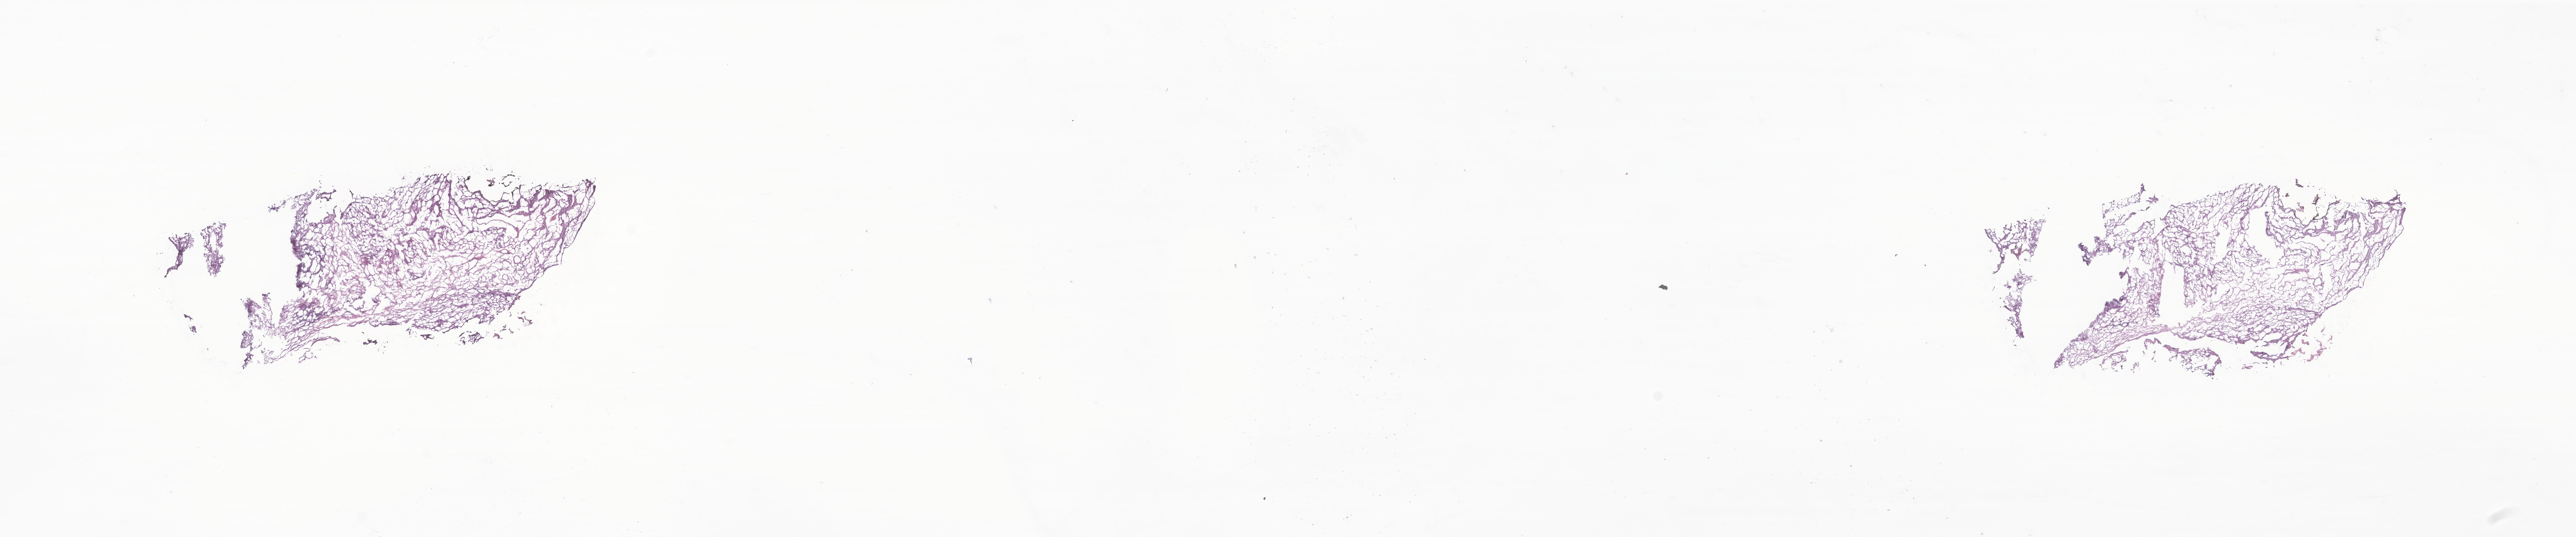
Digitized hematoxylin and eosin (H&E)-stained section of tumor tissue from the orbit — shown as a low-resolution overview of the whole scanned area (about 29.9 x 6.2 mm). Frozen section. Patient: female, age 138 months.
* diagnosis: Embryonal rhabdomyosarcoma, NOS